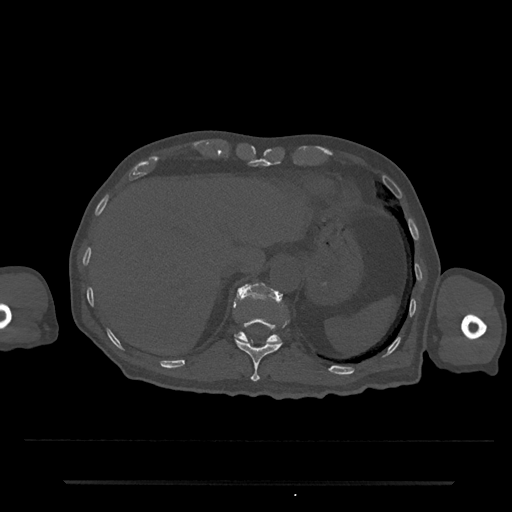
CT including the spine, one axial slice. Slice 237 of 797 in the series (ordered by position). Reconstruction kernel Br40s/3. 120 kVp. Bone window (W 1800 / L 400 HU). 512 × 512 image matrix, field of view 427 × 427 mm. Male patient, age 74 years. From the clinical record (not read from this slice): primary cancer: prostate.
Structures marked on this image (semi-automatic segmentation, software-assisted and operator-edited):
- T11 vertebra: box from (x=234, y=319) to (x=282, y=382) px
- T12 vertebra: (x=235, y=282)–(x=282, y=344)